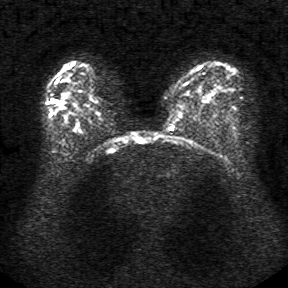
Breast MRI, one axial slice; position 23 of 34 along the scan axis; diffusion-weighted series; image 2 of 4 stored at this slice position (different b-values; order by instance number); 1.5 T; 5 mm slice thickness; 288 × 288 image matrix. Female patient.
Outlined on this slice (outlined manually by an expert reader):
- tumour on diffusion-weighted imaging: box from (x=60, y=105) to (x=64, y=108) px